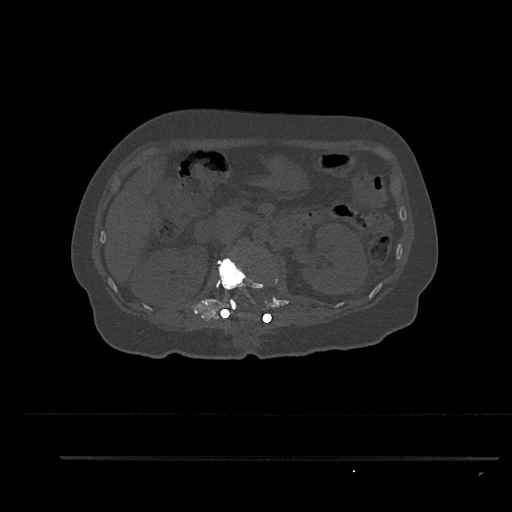
CT including the spine, one axial slice; position 198 of 797 along the scan axis; bone window (W 1800 / L 400 HU); 0.5 mm slice thickness; 512 × 512 image matrix, field of view 408 × 408 mm. Patient: female, 44 years. Case-level facts recorded for this patient, not image findings: primary cancer: renal; vertebrae with lytic lesions (as recorded): L1.
Structures marked on this image (semi-automatic segmentation, software-assisted and operator-edited):
- L1 vertebra: bounding box (x1, y1, x2, y2) in pixels: (218, 257, 279, 317)
- L2 vertebra: (224, 304, 228, 310)